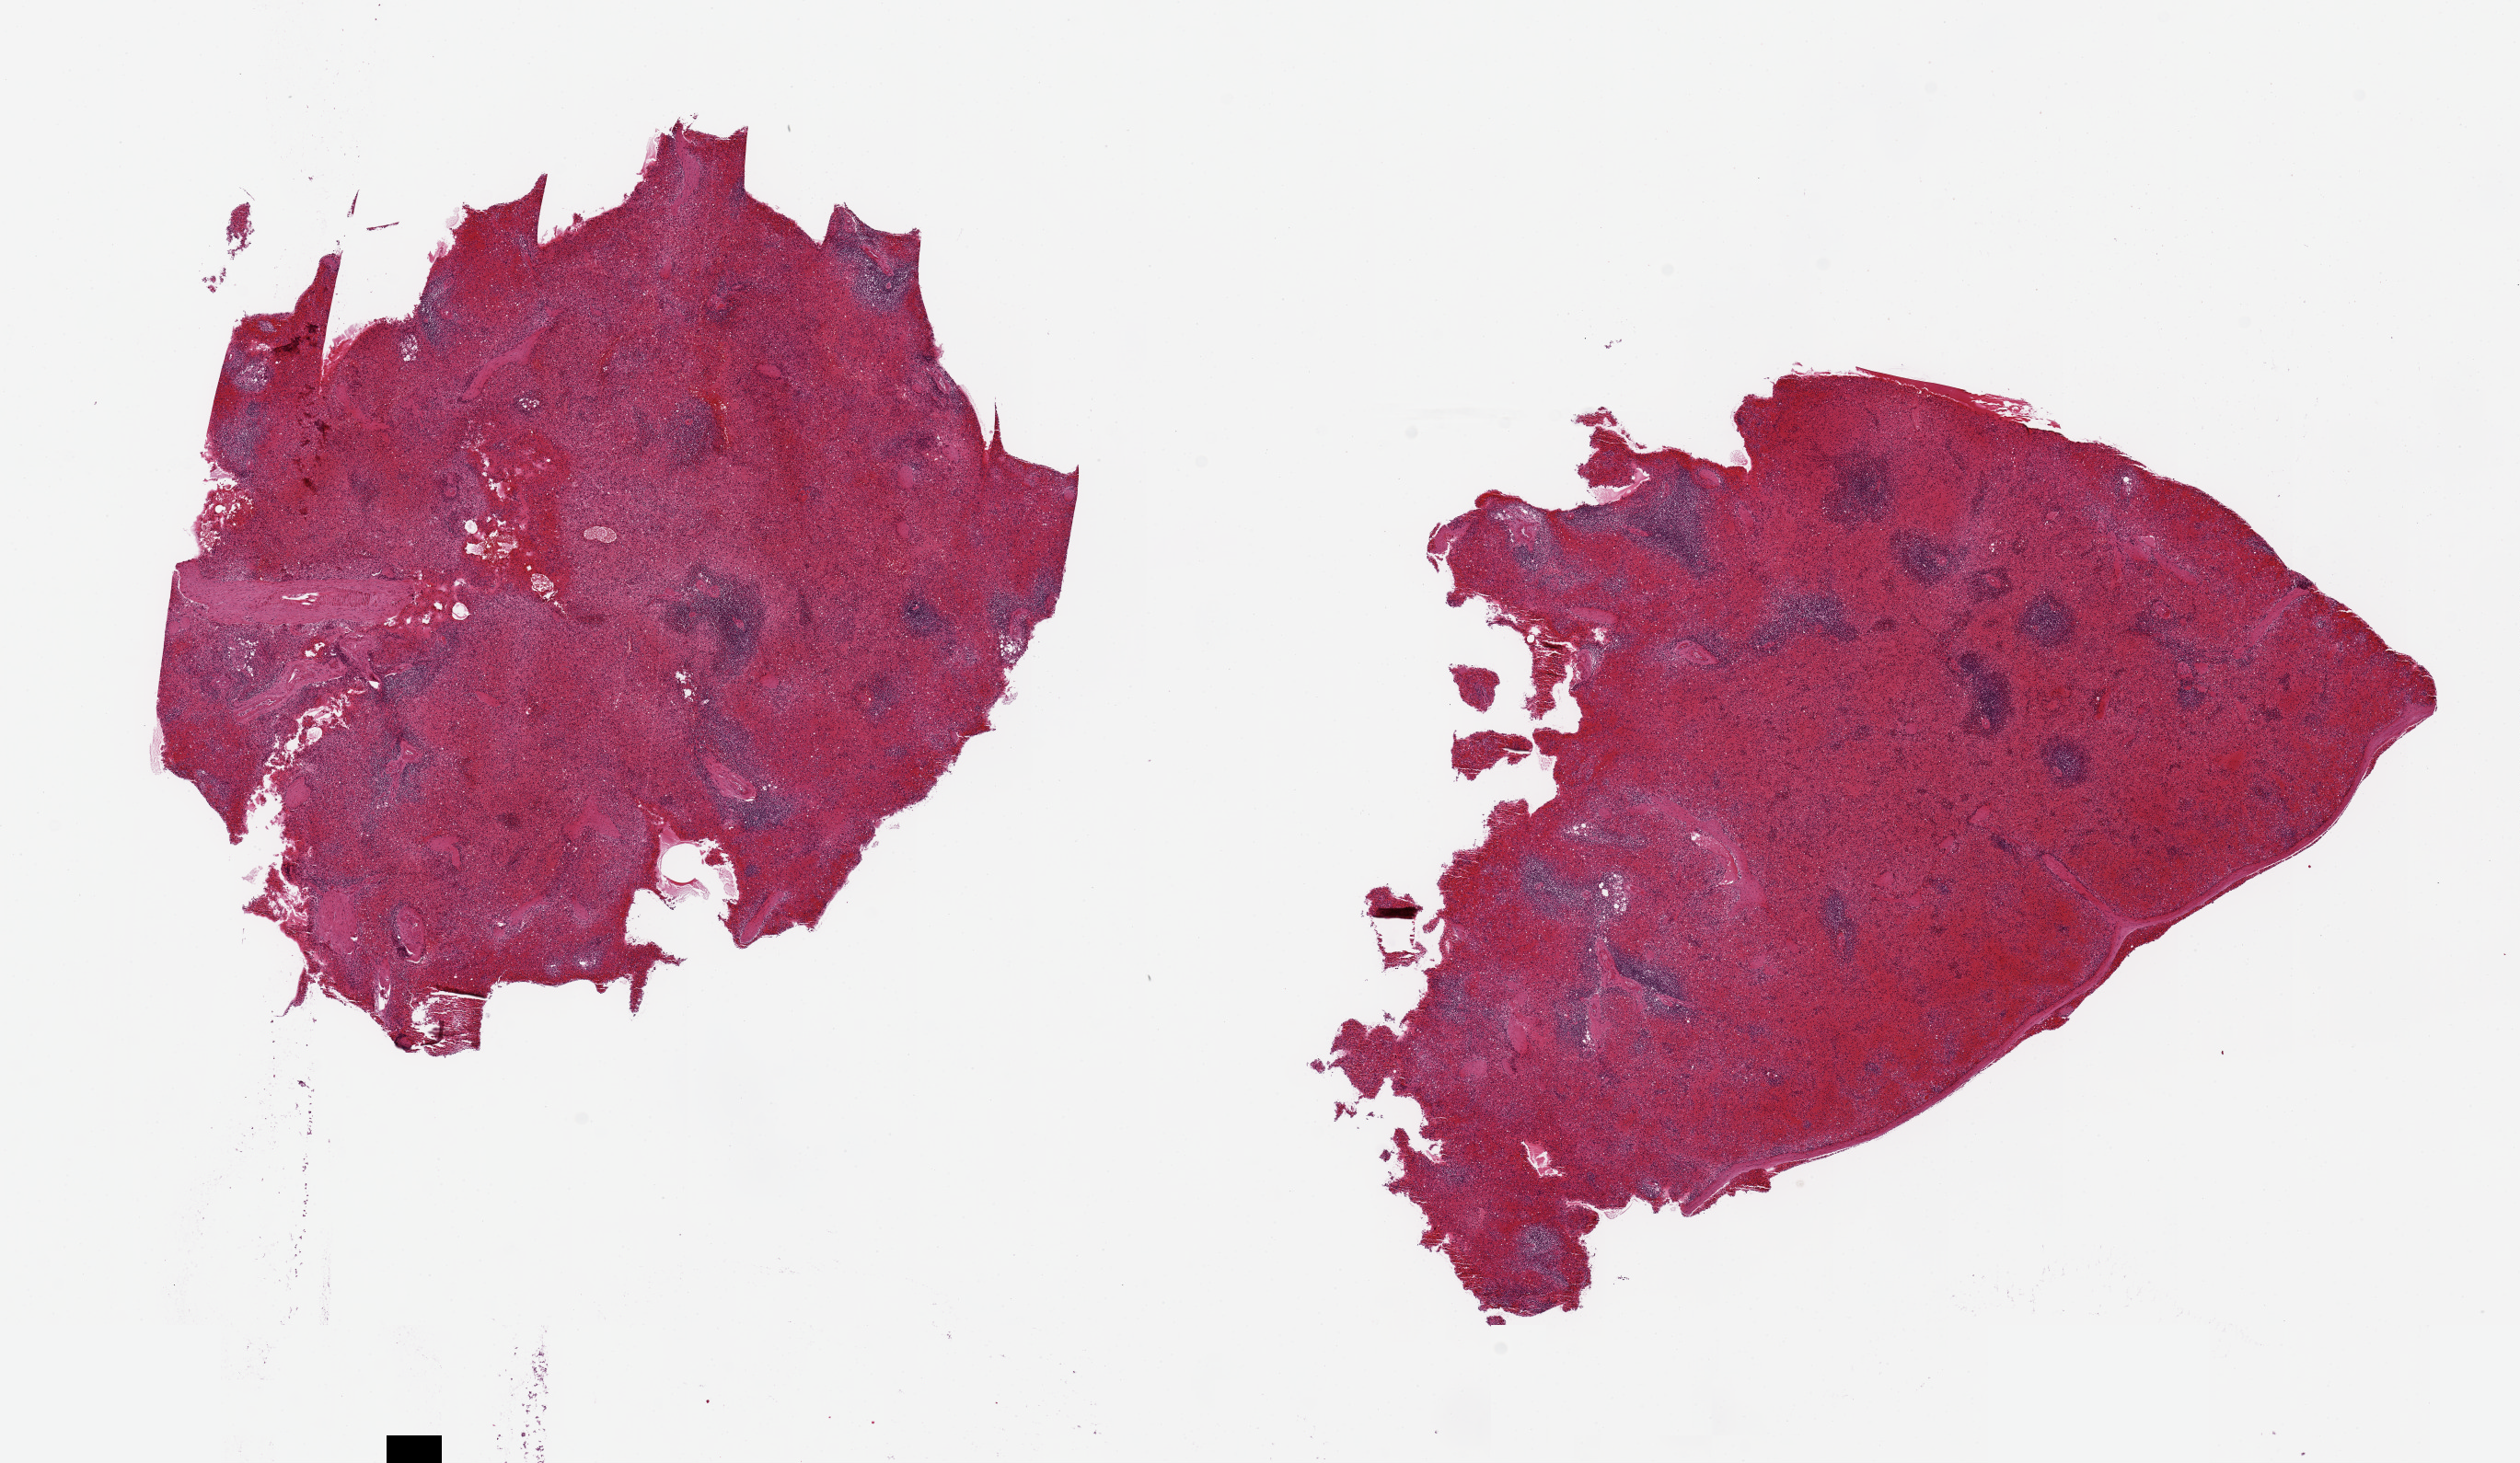
H&E whole-slide image, a low-resolution overview of the entire scanned area, about 21.7 x 12.6 mm (slide scanned at 20x), PAXgene-fixed, paraffin-embedded tissue, sampled site (target tissue): spleen, donor tissue sample. Donor sex: male.
Review note (as recorded): 2 pieces 8x8 & 10x7mm; marked congestion, poorly preserved.